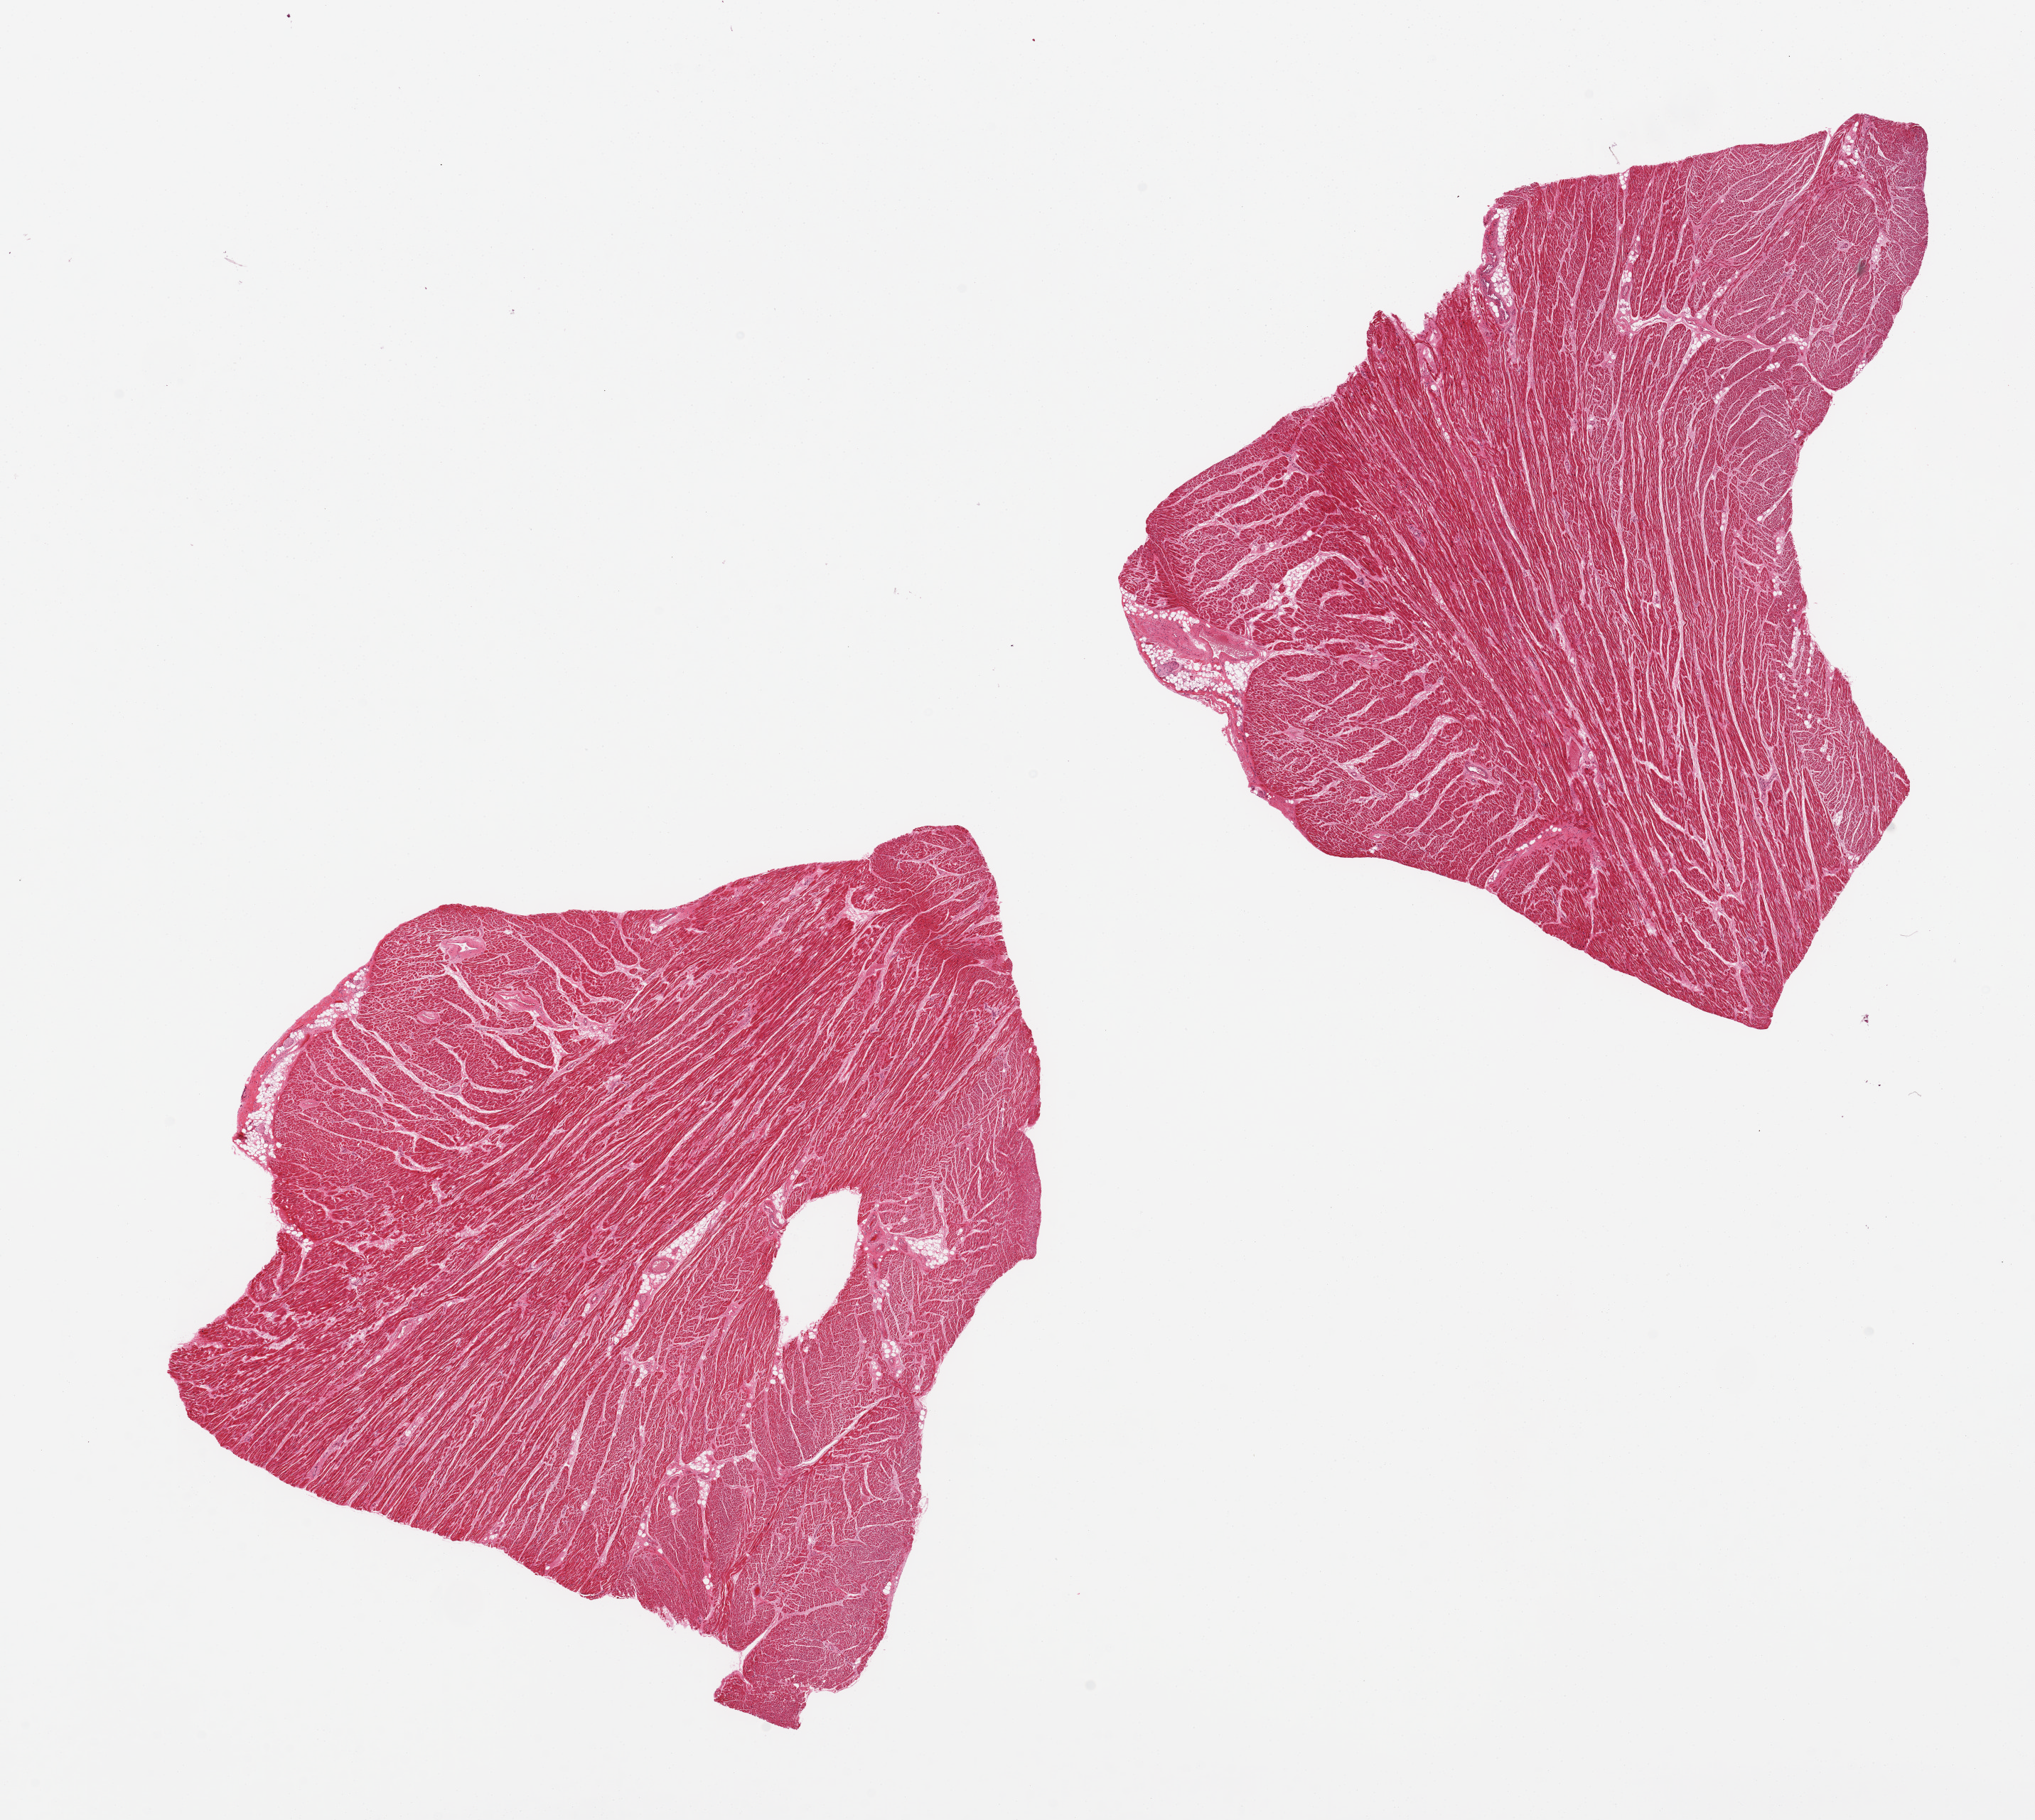
Digitized hematoxylin and eosin (H&E)-stained section, a low-resolution overview of the entire scanned area, about 22.6 x 20.3 mm, PAXgene-fixed, paraffin-embedded tissue, target tissue: heart, tissue donor sample. Male donor.
Reviewer comment on this tissue sample: 2 pieces, small attachment of fat, vessel, and nerve.